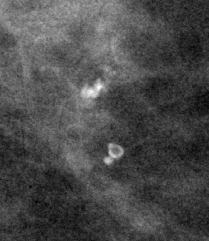
Cropped region of a digitized screen-film mammogram centred on a radiologist-marked abnormality, right breast, CC view.
Calcifications, morphology pleomorphic, distribution clustered; BI-RADS assessment category 2; subtlety rating 4 on a 1 (subtle) to 5 (obvious) scale; benign; no additional work-up was recommended (benign without callback).